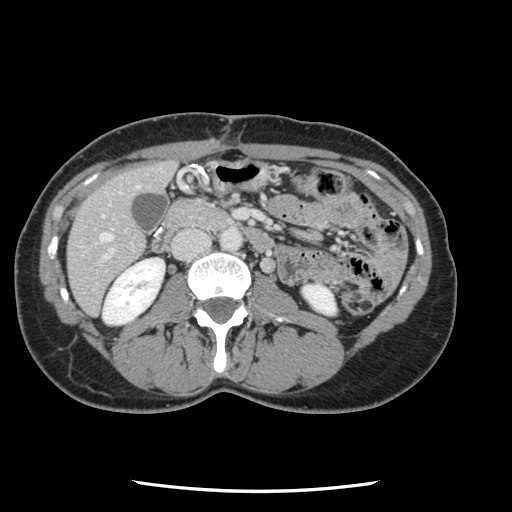
Contrast-enhanced abdominal CT, one axial slice. Slice 32 of 134 in the series (ordered by position). 120 kVp. Intravenous contrast given. Soft-tissue window (W 400 / L 40 HU). 2.5 mm slice thickness. 512 × 512 image matrix, field of view 330 × 330 mm. Female patient, age 43 years. From the clinical record (not read from this slice): diagnosis: colorectal cancer liver metastases, imaged before liver resection; multiple liver metastases: yes; largest metastasis: 3.4 cm; disease in both lobes: yes.
Structures marked on this image (manually delineated by an expert):
- hepatic veins: bounding box <100,186,138,241> (left, top, right, bottom; pixels)
- liver: <68,162,176,315>
- planned liver remnant (the part of the liver to remain after resection): <68,162,176,315>